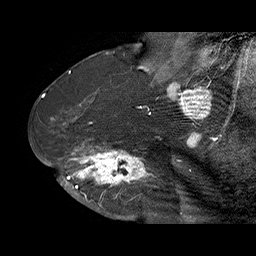
Breast MRI (dynamic contrast-enhanced), one sagittal slice. Position 41 of 70 along the scan axis. Dynamic contrast-enhanced series, time point 2 of 6 at this slice position (early post-contrast). 1.5 T. TE 4.5 ms, TR 32.4 ms. 3 mm slice thickness. 256 × 256 image matrix. Female patient. Case-level facts recorded for this patient, not image findings: setting: breast cancer imaged before/during neoadjuvant chemotherapy; receptor status: HR-positive, HER2-negative.
Structures marked on this image (semi-automatically segmented with operator editing):
- analysis volume of interest (the breast-tissue region the enhancement analysis was run in; not a lesion): bounding box [x1, y1, x2, y2] px = [71, 128, 159, 202]
- tumour enhancement mask (voxels above the 100 % enhancement threshold inside the analysis volume of interest): [71, 139, 155, 202]